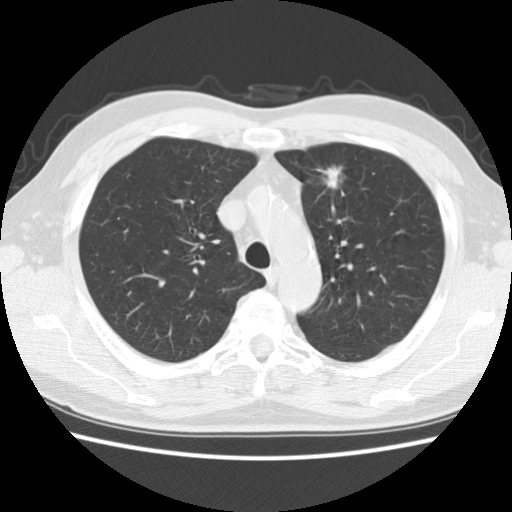
Low-dose screening chest CT, one axial slice; reconstruction kernel STANDARD; lung window (W 1500 / L -600 HU); 2.5 mm slice thickness; 512 × 512 image matrix, field of view 337 × 337 mm.
Structures marked on this image (expert manual segmentation):
- lesion 1 (tumor, upper lobe of left lung): bounding box (x1, y1, x2, y2) in pixels: (316, 166, 342, 192)